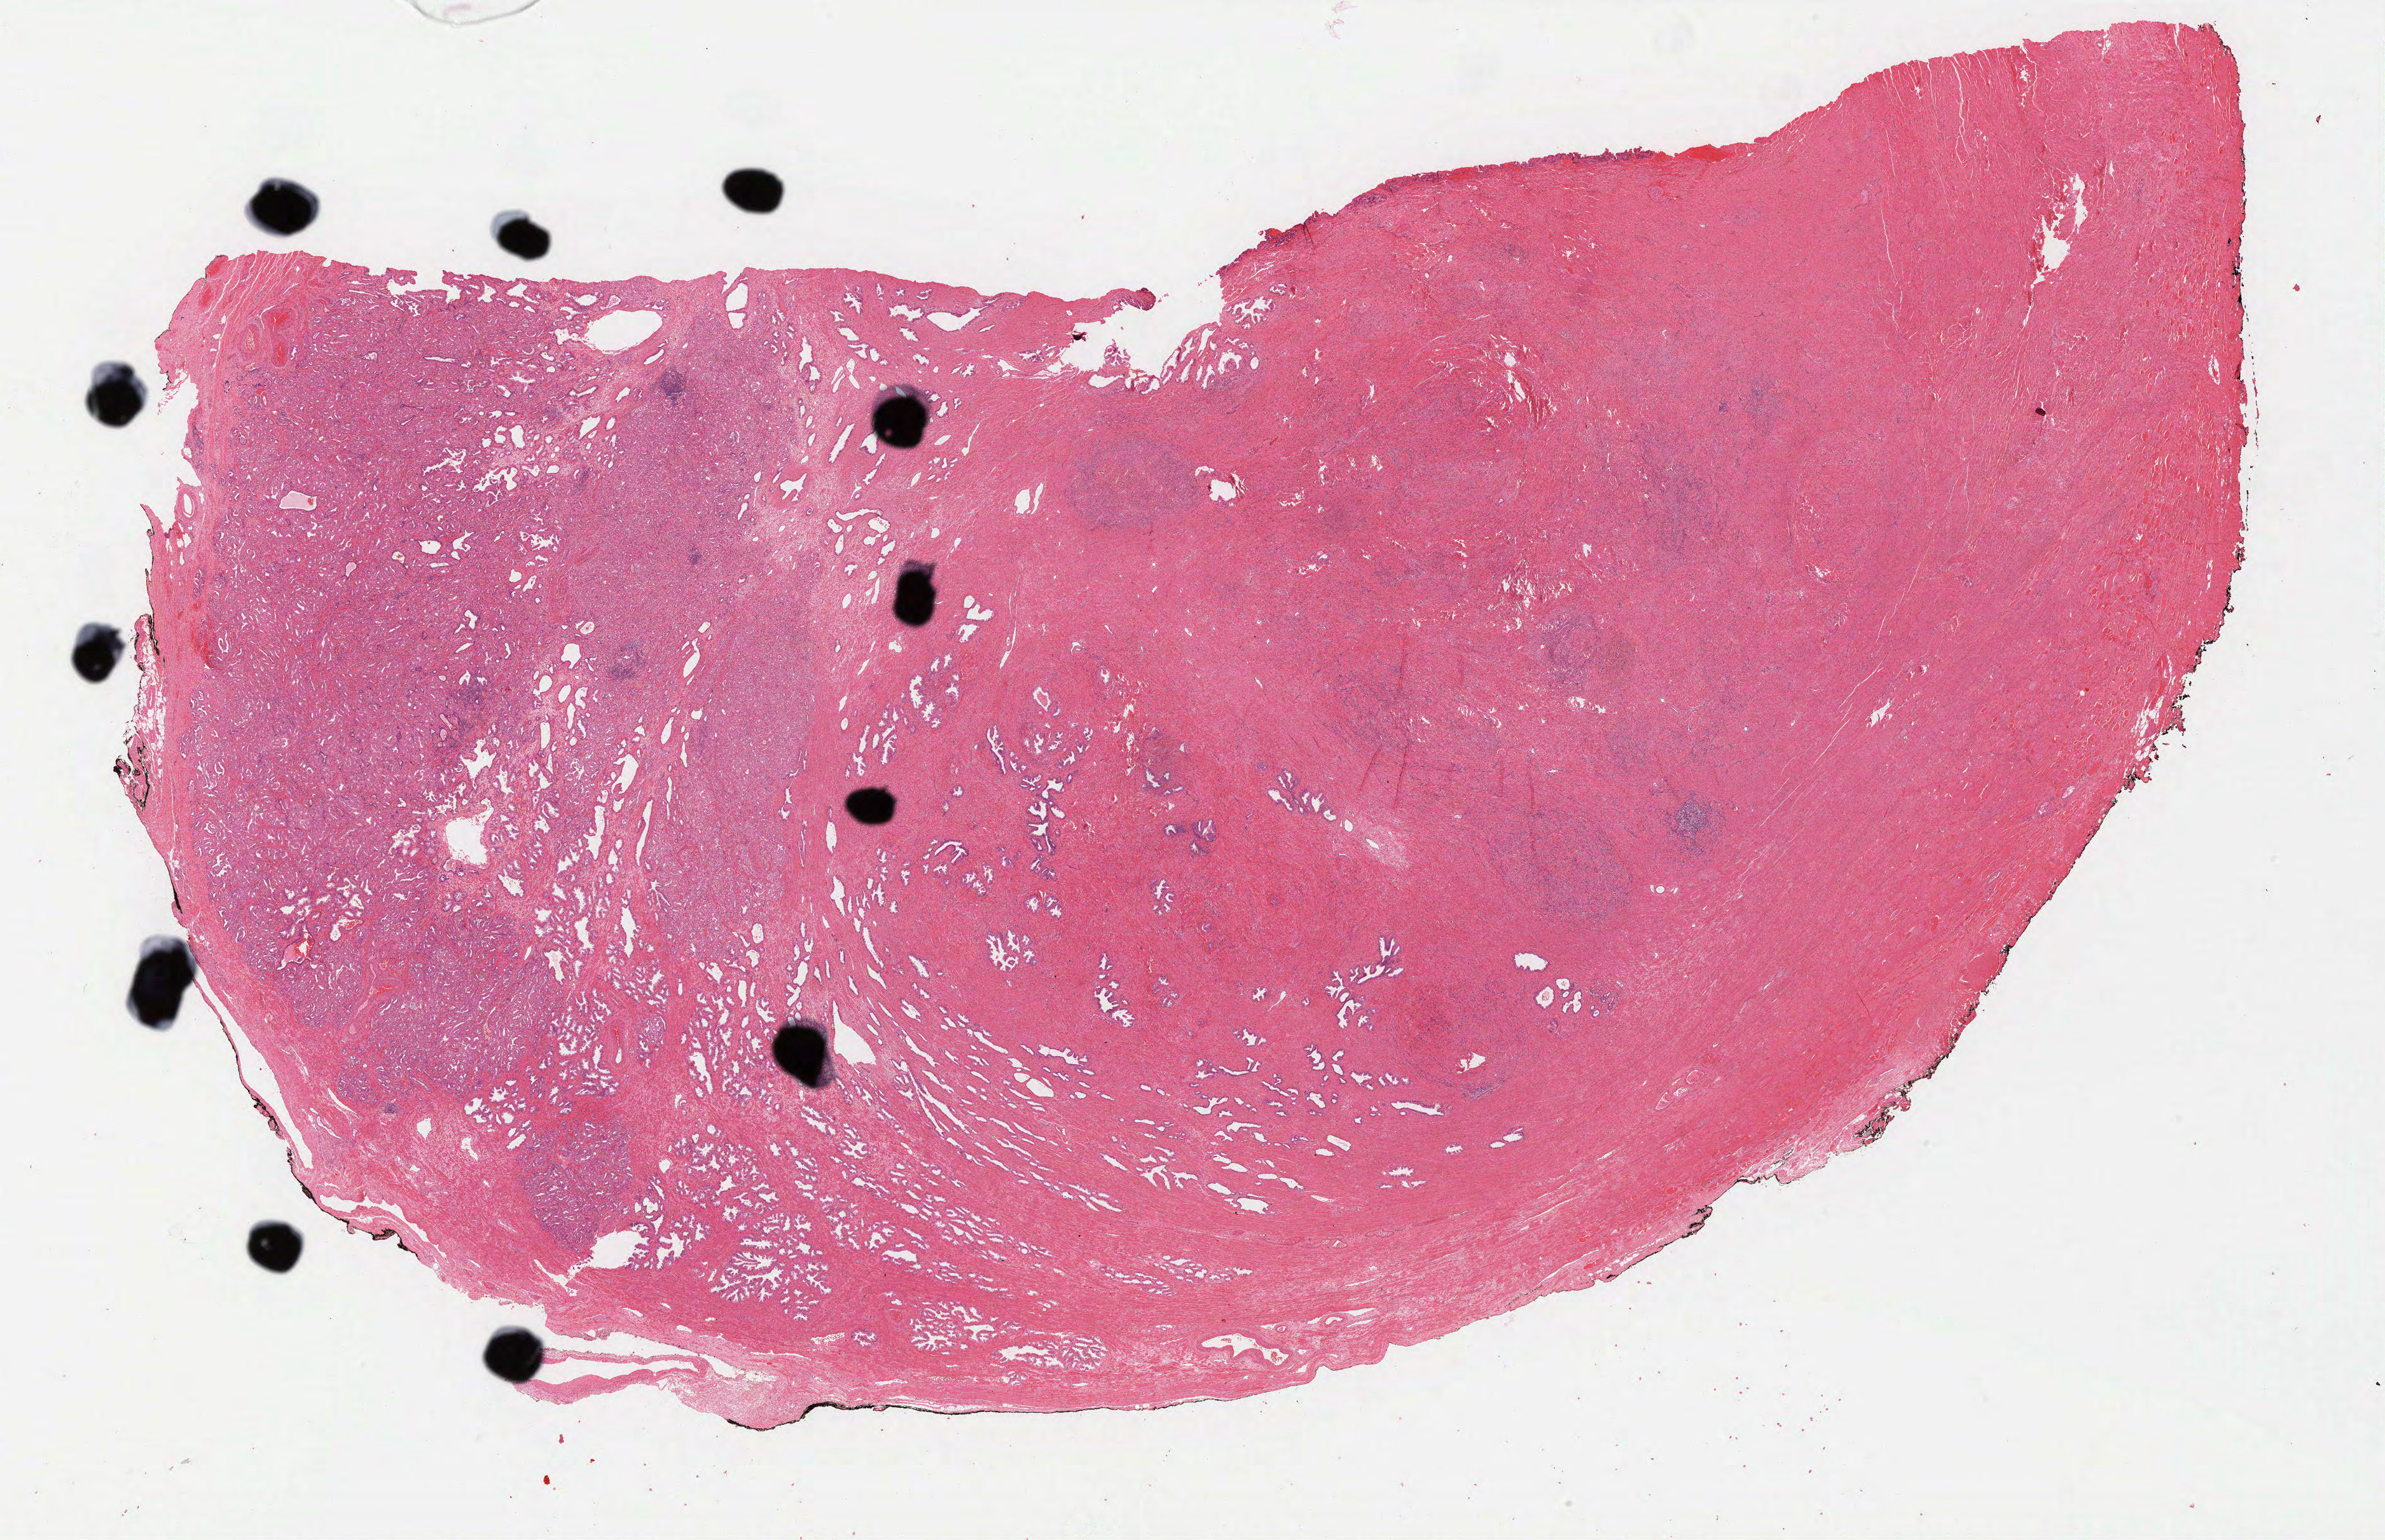
Hematoxylin and eosin (H&E) stained whole-slide image — low-resolution overview of the scanned area, about 30.0 x 19.4 mm (slide scanned at 40x), formalin-fixed paraffin-embedded (FFPE) diagnostic section, sample: primary tumour, prostate. Male, age 56 years at initial diagnosis. Gleason score: 7 (3+4).
• lymph nodes positive (case pathology): 1 of 11 examined
• pathologic diagnosis: Adenocarcinoma, NOS